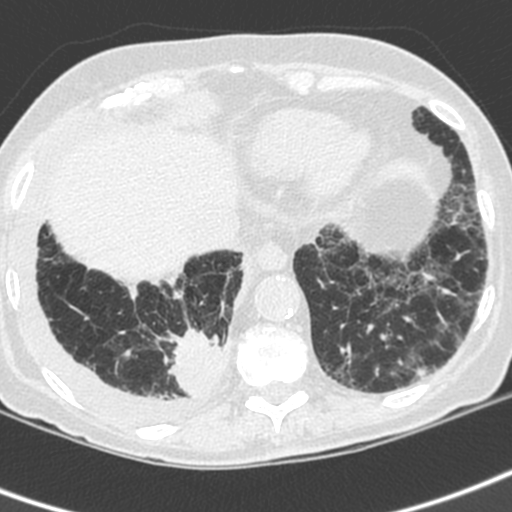
Axial slice from a low-dose chest CT screening exam. Baseline annual screen. Lung window (W 1500 / L -600 HU). 1.3 mm slice thickness. 120 kVp. Slice 151 of 192 in the series. 512 × 512 image matrix. Female, age 73 years at enrolment. Current smoker at enrolment.
- Lesion marked by an expert reader, bounding box (x1, y1, x2, y2) in pixels: (159, 324, 235, 405).
- The exam's reader record, not a measurement of the box and not confirmed to be the same lesion: non-calcified nodule or mass ≥4 mm, right lower lobe, 35 × 30 mm, spiculated (stellate) margins, soft tissue attenuation.
- Official screen result: positive, change unspecified: nodule(s) >= 4 mm or enlarging nodule(s), mass(es), or other non-specific abnormalities suspicious for lung cancer.
- Participant outcome: lung cancer diagnosed 22 days after this screen — adenocarcinoma, NOS, right lower lobe, stage IV (AJCC 6th edition), 35 mm at pathology.